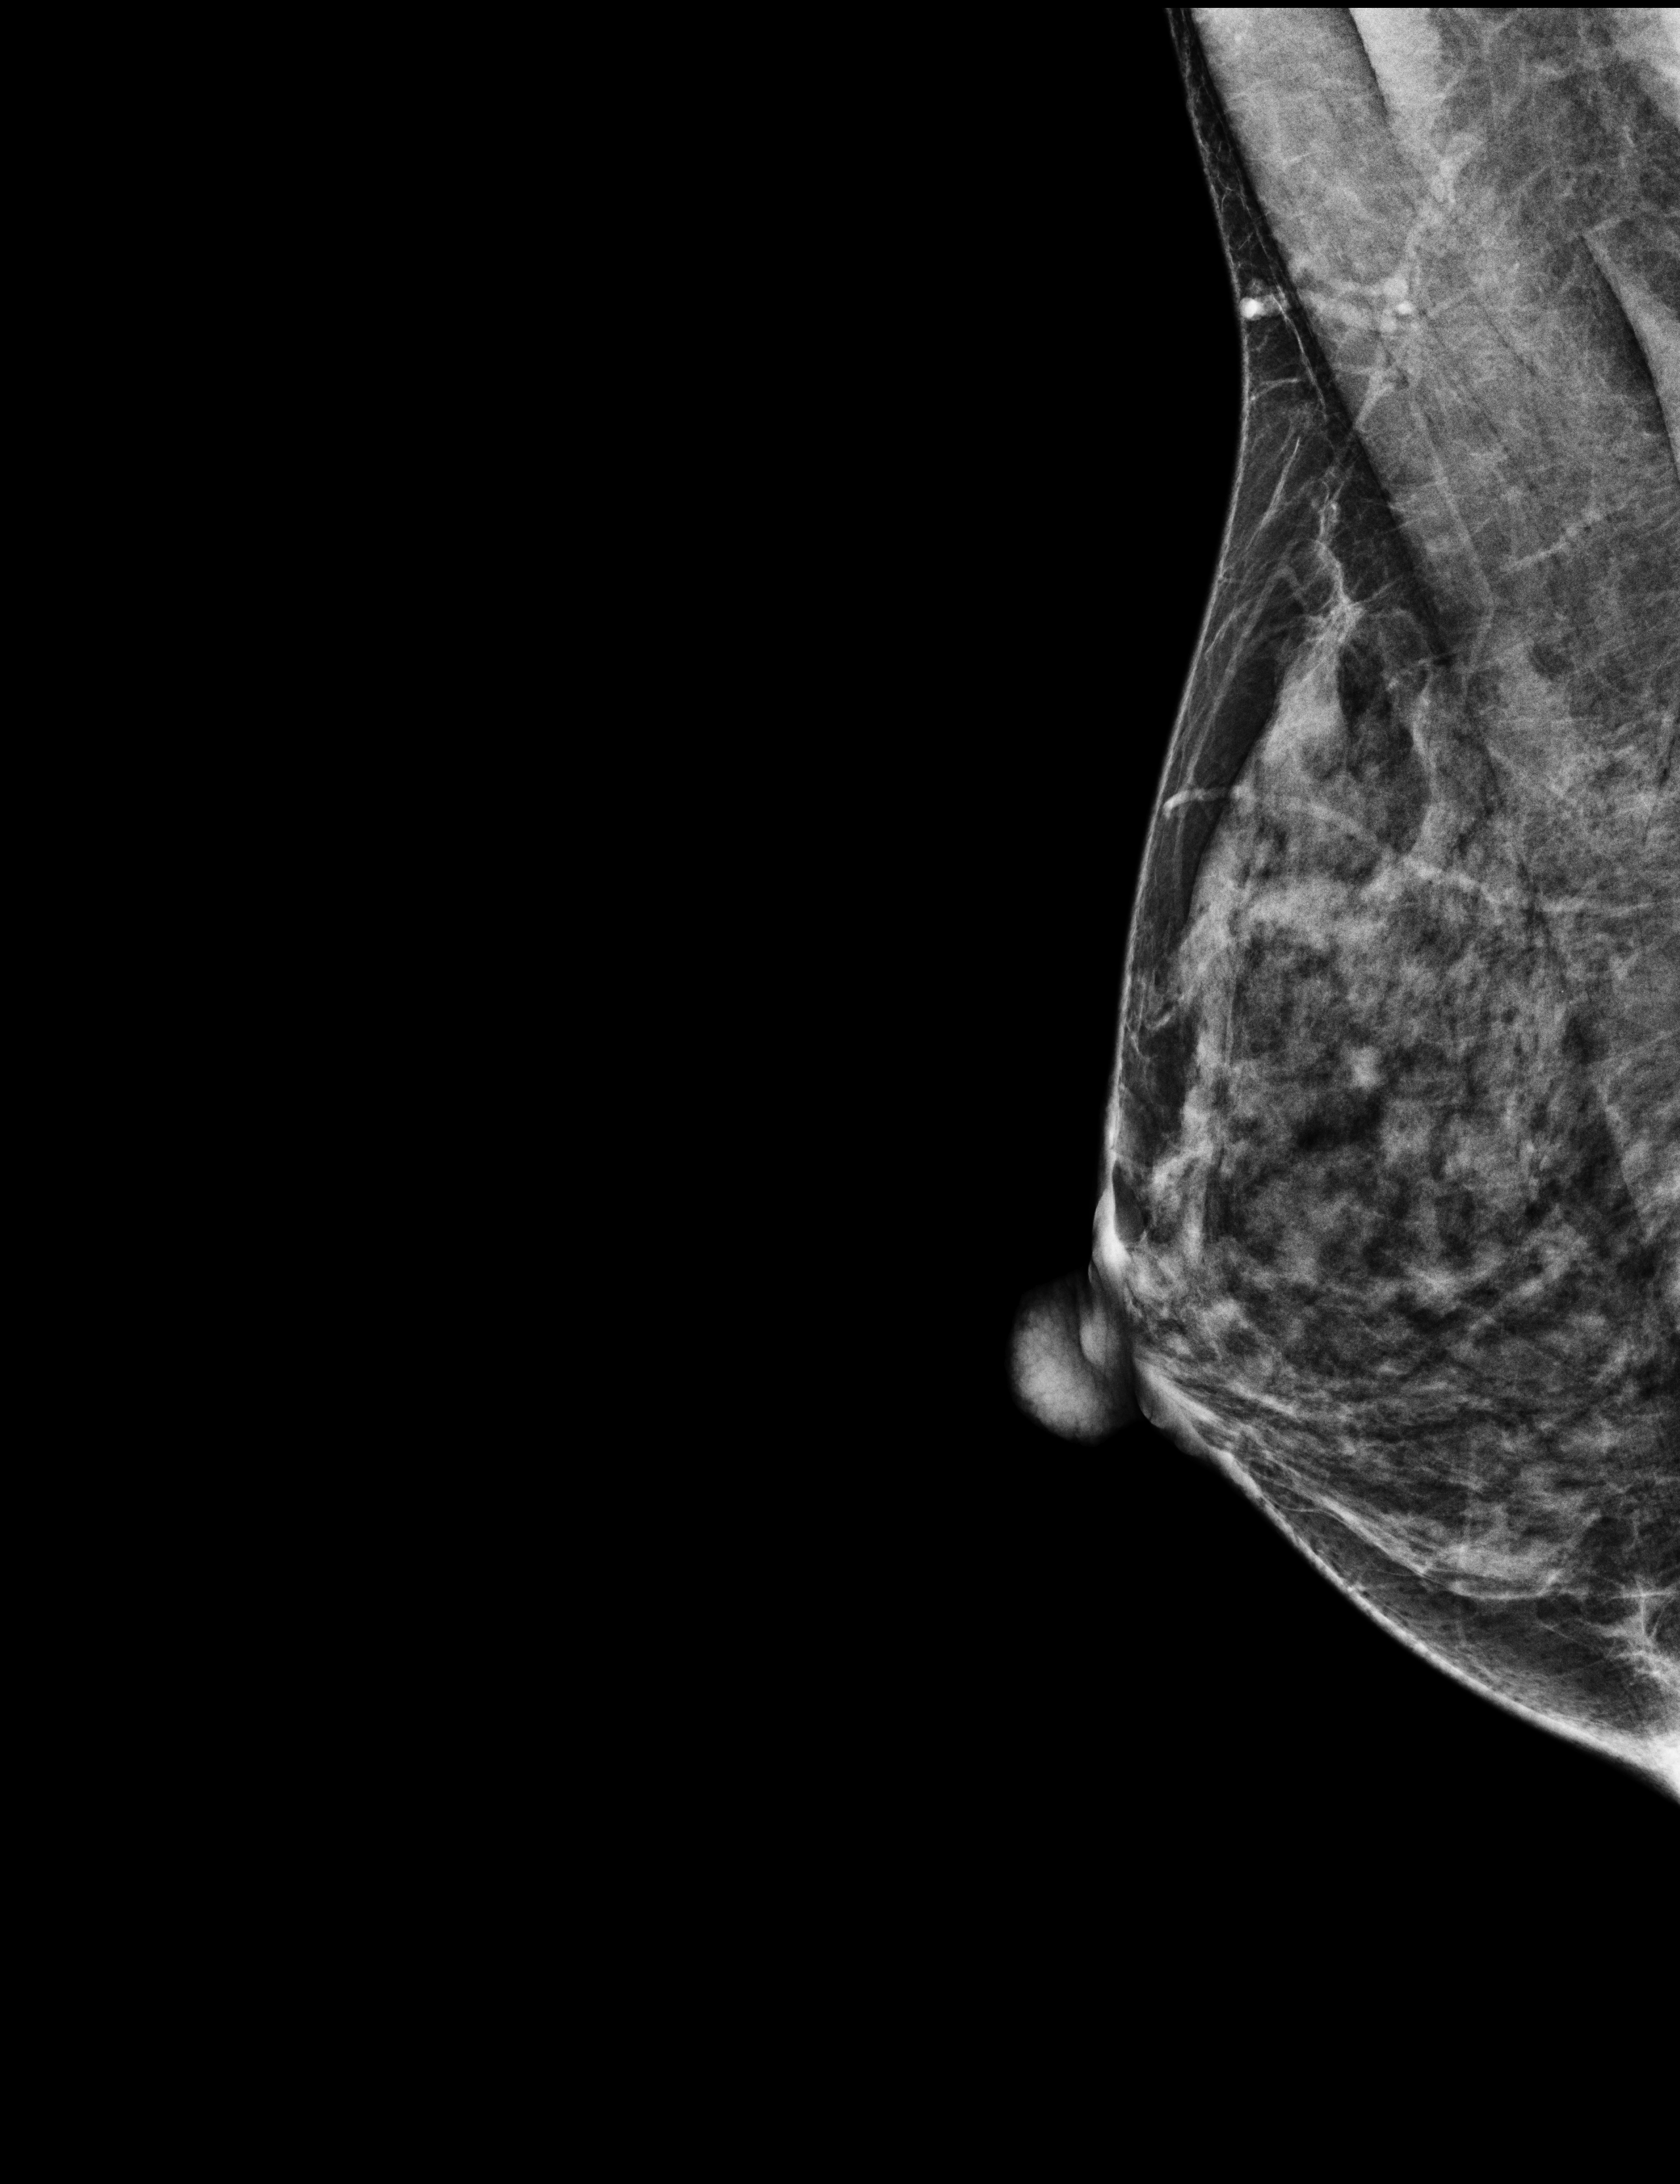
Screening examination. Patient: female, 43 years.
Image type: full-field digital mammogram. Breast: right. Projection: mediolateral oblique (MLO) view.